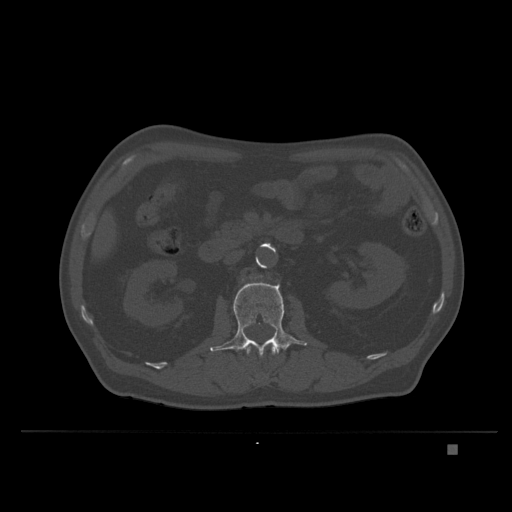
CT including the spine, one axial slice; slice 120 of 435 in the series (ordered by position); bone window (W 1800 / L 400 HU); 1.5 mm slice thickness; 512 × 512 image matrix, field of view 434 × 434 mm. Male patient, age 73 years. From the clinical record (not read from this slice): primary cancer: skin.
Structures marked on this image (semi-automatically segmented with operator editing):
- L1 vertebra: box from (x=246, y=343) to (x=277, y=378) px
- L2 vertebra: (x=210, y=282)–(x=307, y=357)